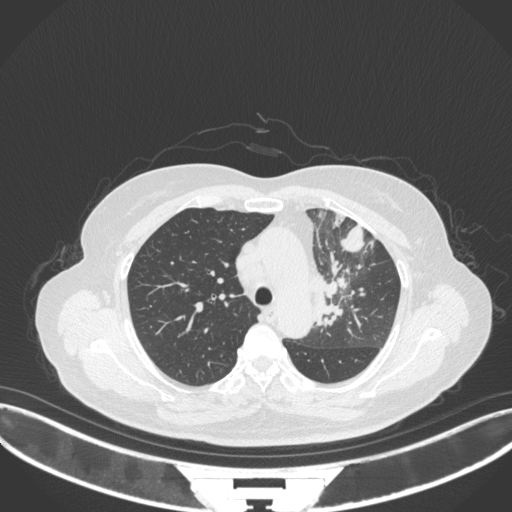
Chest CT, one axial slice. Slice 243 of 382 in the series (ordered by position). Reconstruction kernel B31f. 120 kVp. Lung window (W 1500 / L -600 HU). 1 mm slice thickness. 512 × 512 image matrix. Female patient, age 64 years. Case-level facts recorded for this patient, not image findings: clinical TNM (as recorded): T2a N2 M0.
Structures marked on this image (rectangle marked by the reading radiologist):
- lung tumour (recorded histology: adenocarcinoma): bounding box [x1, y1, x2, y2] px = [312, 252, 355, 334]
- lung tumour (recorded histology: adenocarcinoma): [335, 221, 372, 256]